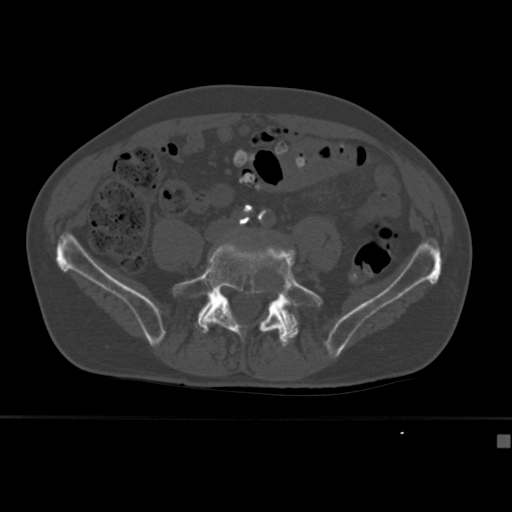
CT including the spine, one axial slice; slice 87 of 430 in the series (ordered by position); 120 kVp; bone window (W 1800 / L 400 HU); 1.5 mm slice thickness; 512 × 512 image matrix, field of view 337 × 337 mm. Male patient, age 64 years. From the clinical record (not read from this slice): primary cancer: uterus; vertebrae with lytic lesions (as recorded): T1, T4, T5, T7, L5.
Structures marked on this image (semi-automatic segmentation, software-assisted and operator-edited):
- L5 vertebra: box from (x=172, y=240) to (x=323, y=347) px